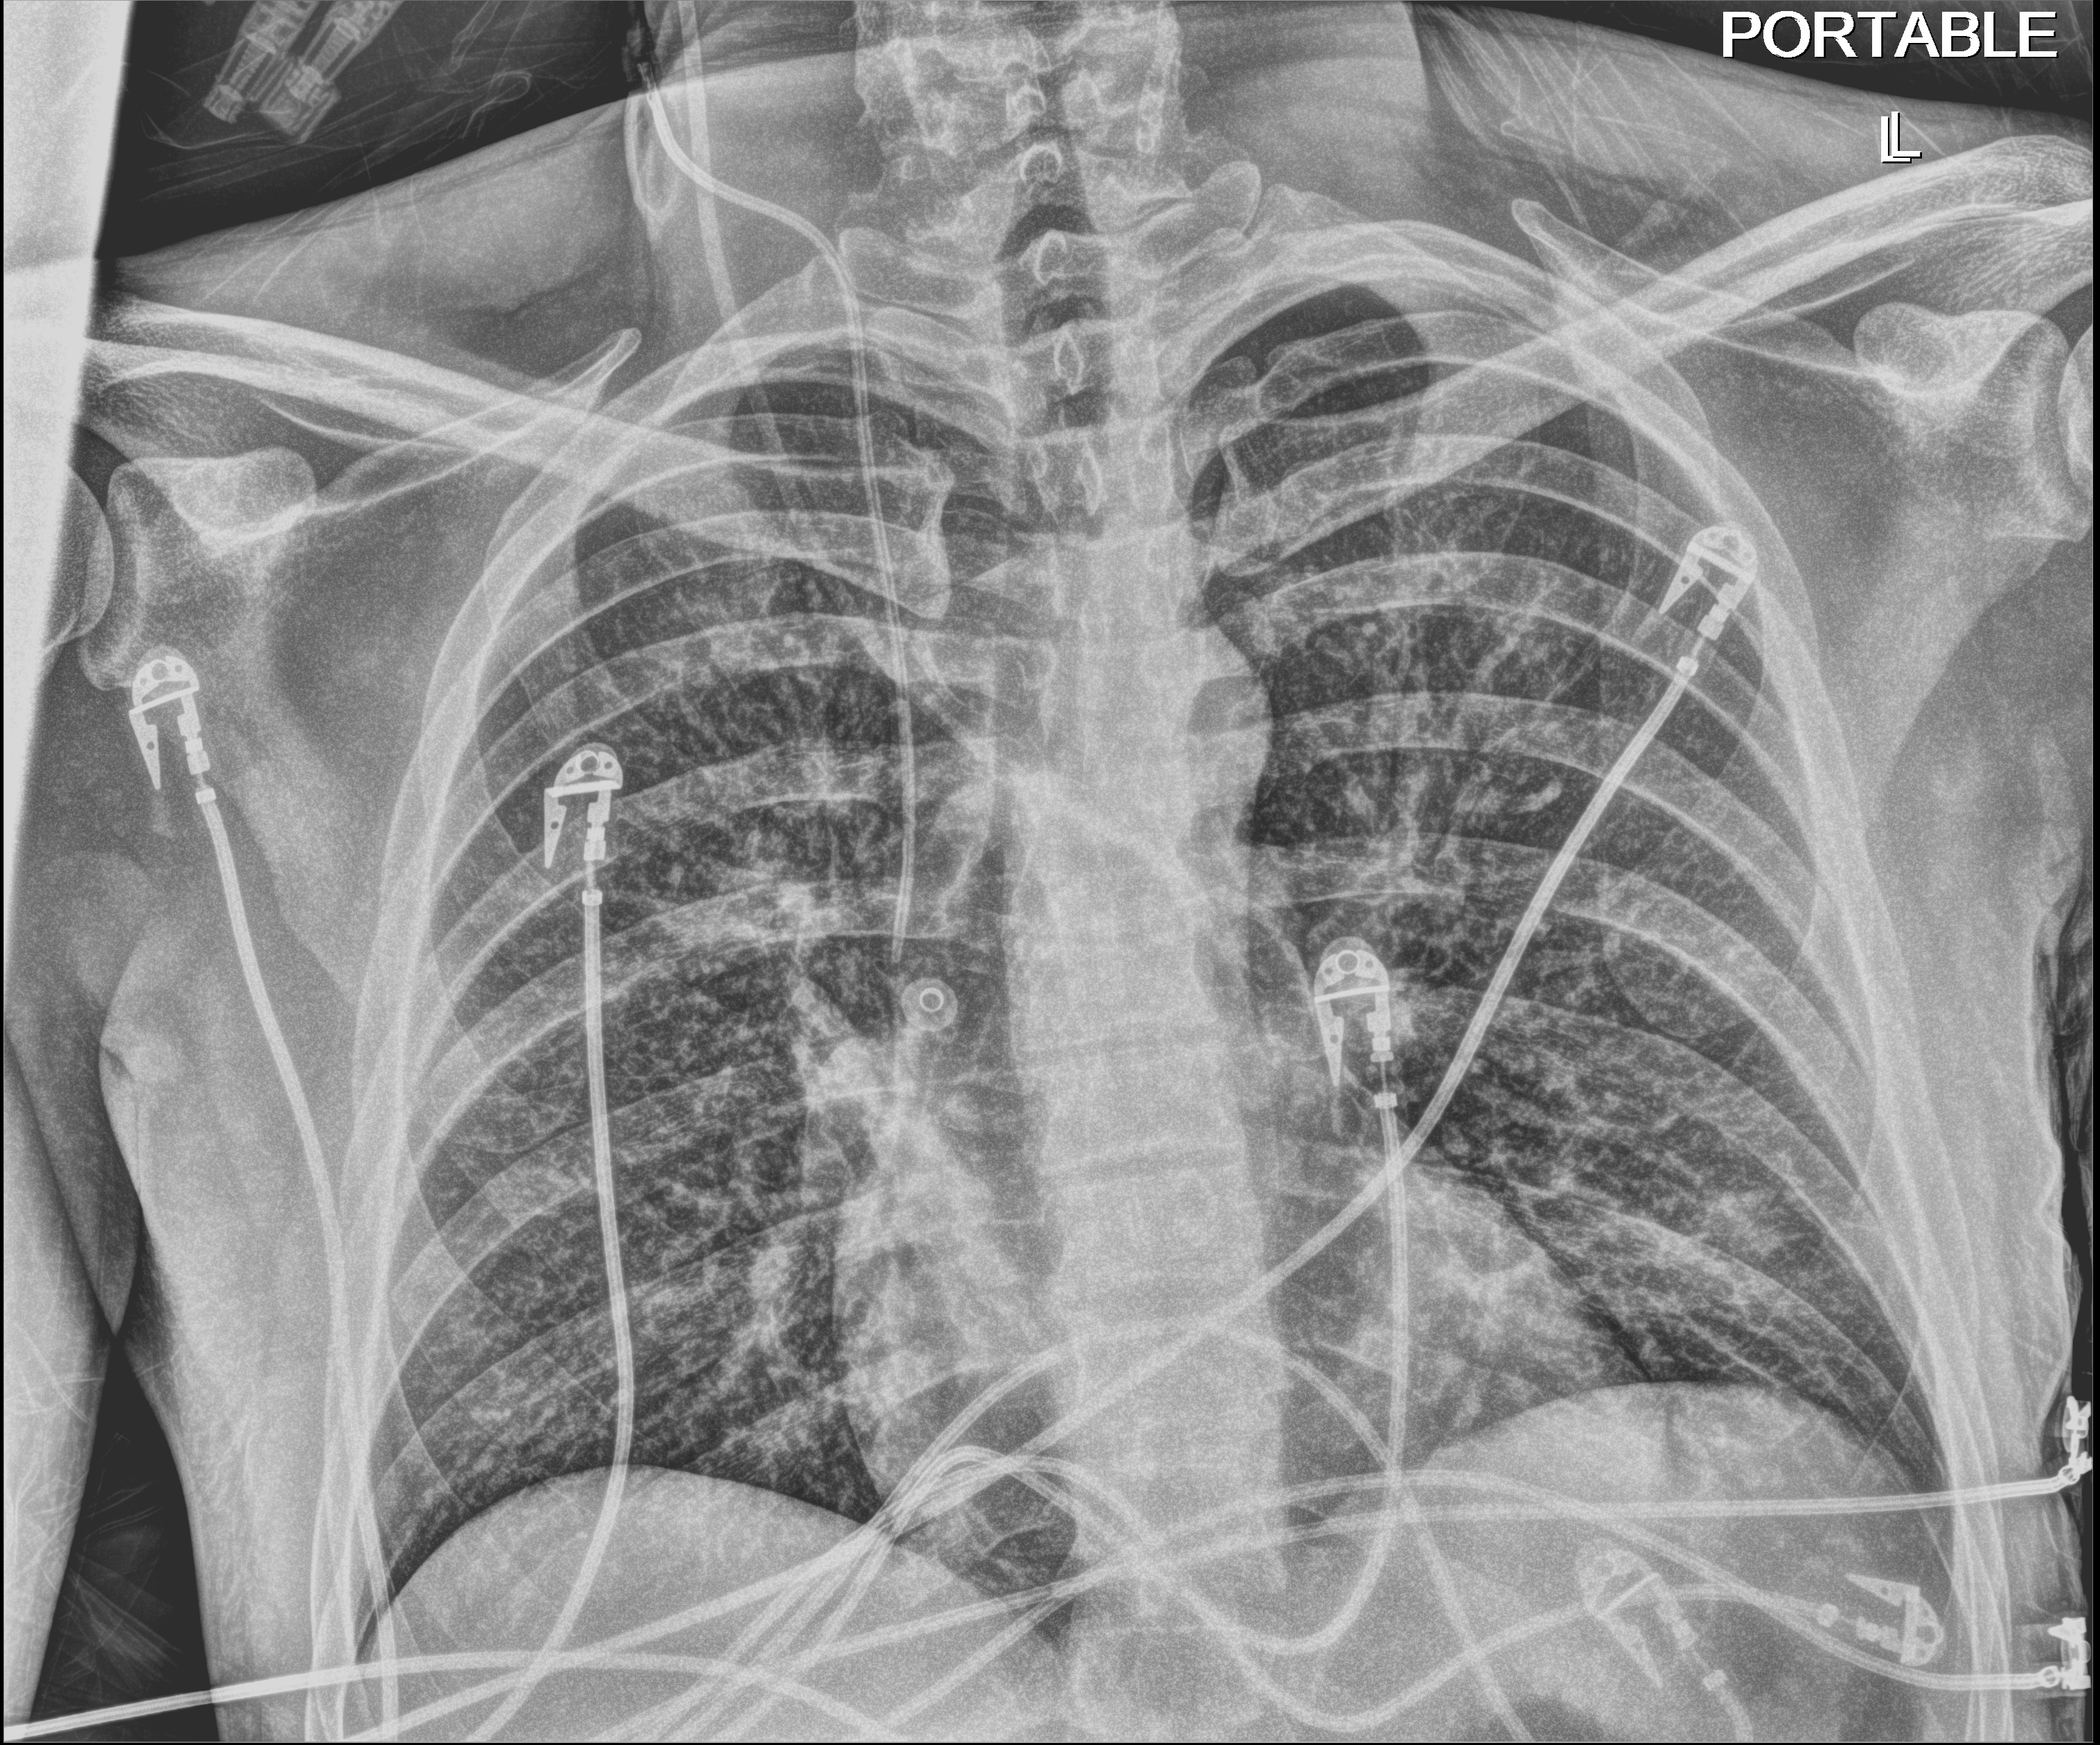
Chest X-ray (portable). Male patient hospitalised with COVID-19, age 18–59 years.
From the hospital-stay record, not from the radiograph (when in the stay this image was taken is not recorded):
- admitted to intensive care during this hospital stay: no
- mechanically ventilated during this hospital stay: yes